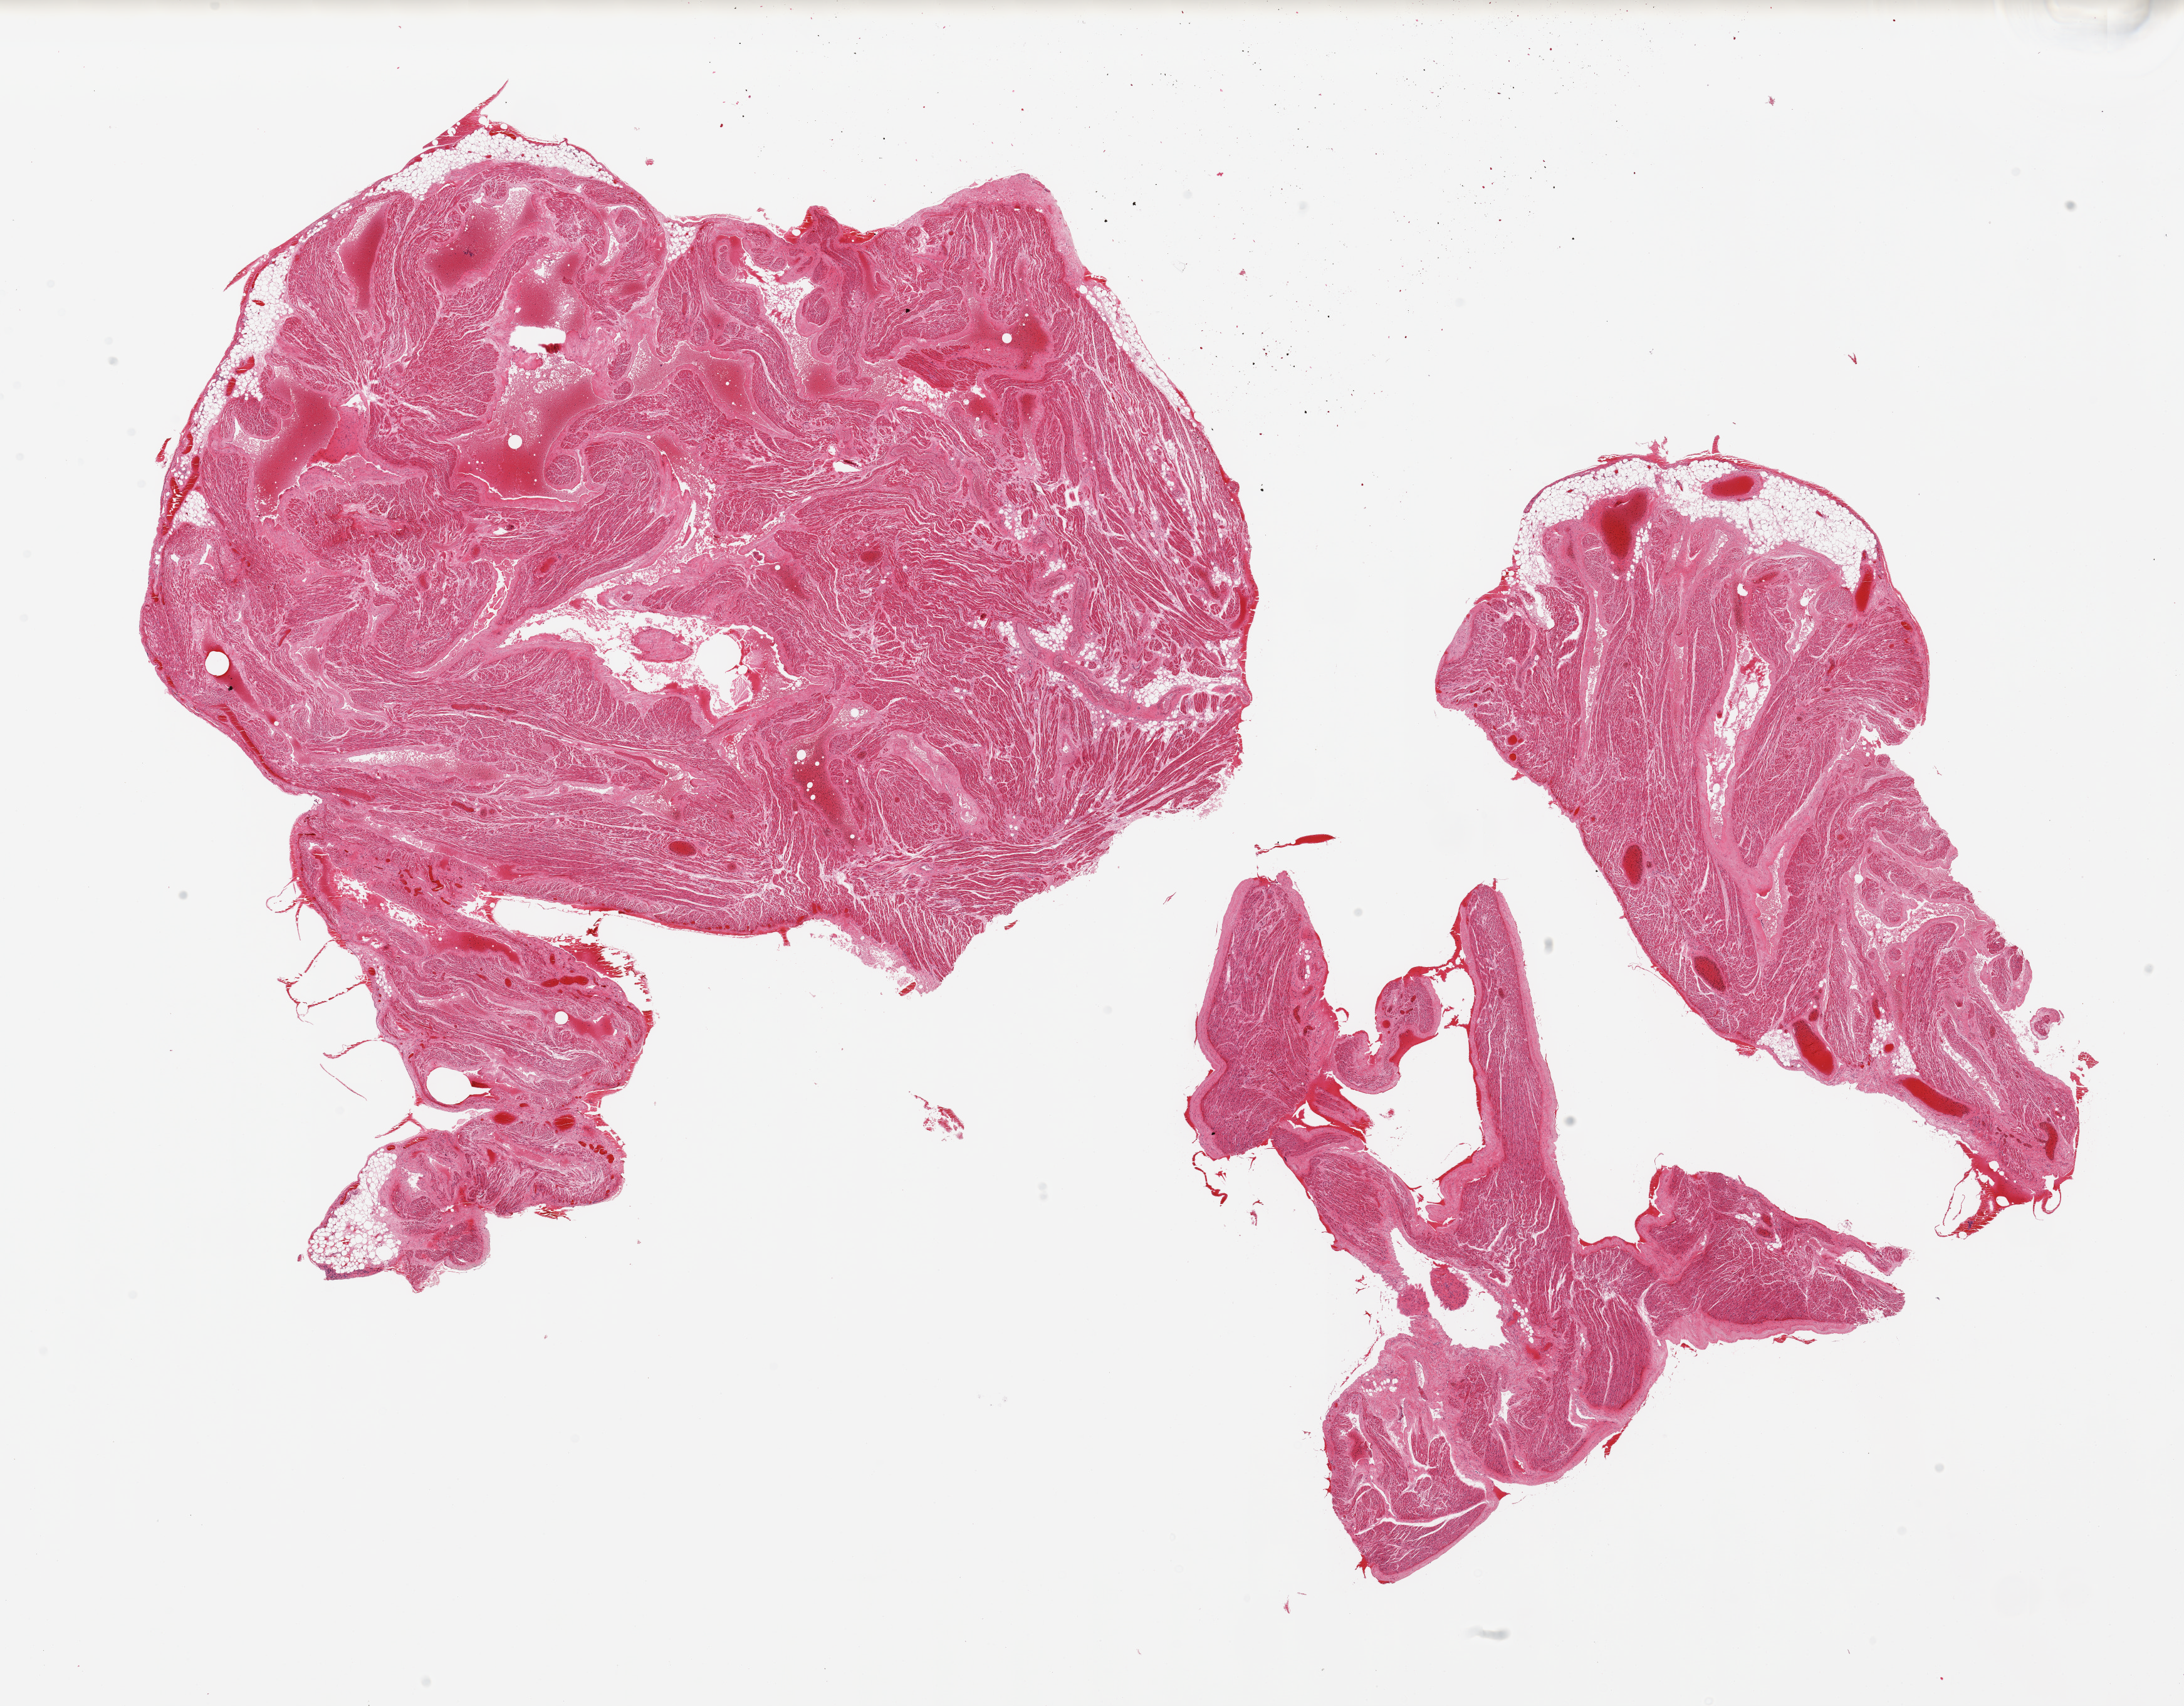
Hematoxylin and eosin (H&E) whole-slide image, brightfield, whole scanned area (about 27.6 x 21.5 mm, slide scanned at 20x) shown as a low-resolution overview; PAXgene-fixed paraffin-embedded (PFPE) section; section of auricular appendage (target tissue); tissue donor sample. Male donor.
Review note (as recorded): 2 pieces; <5% fat.